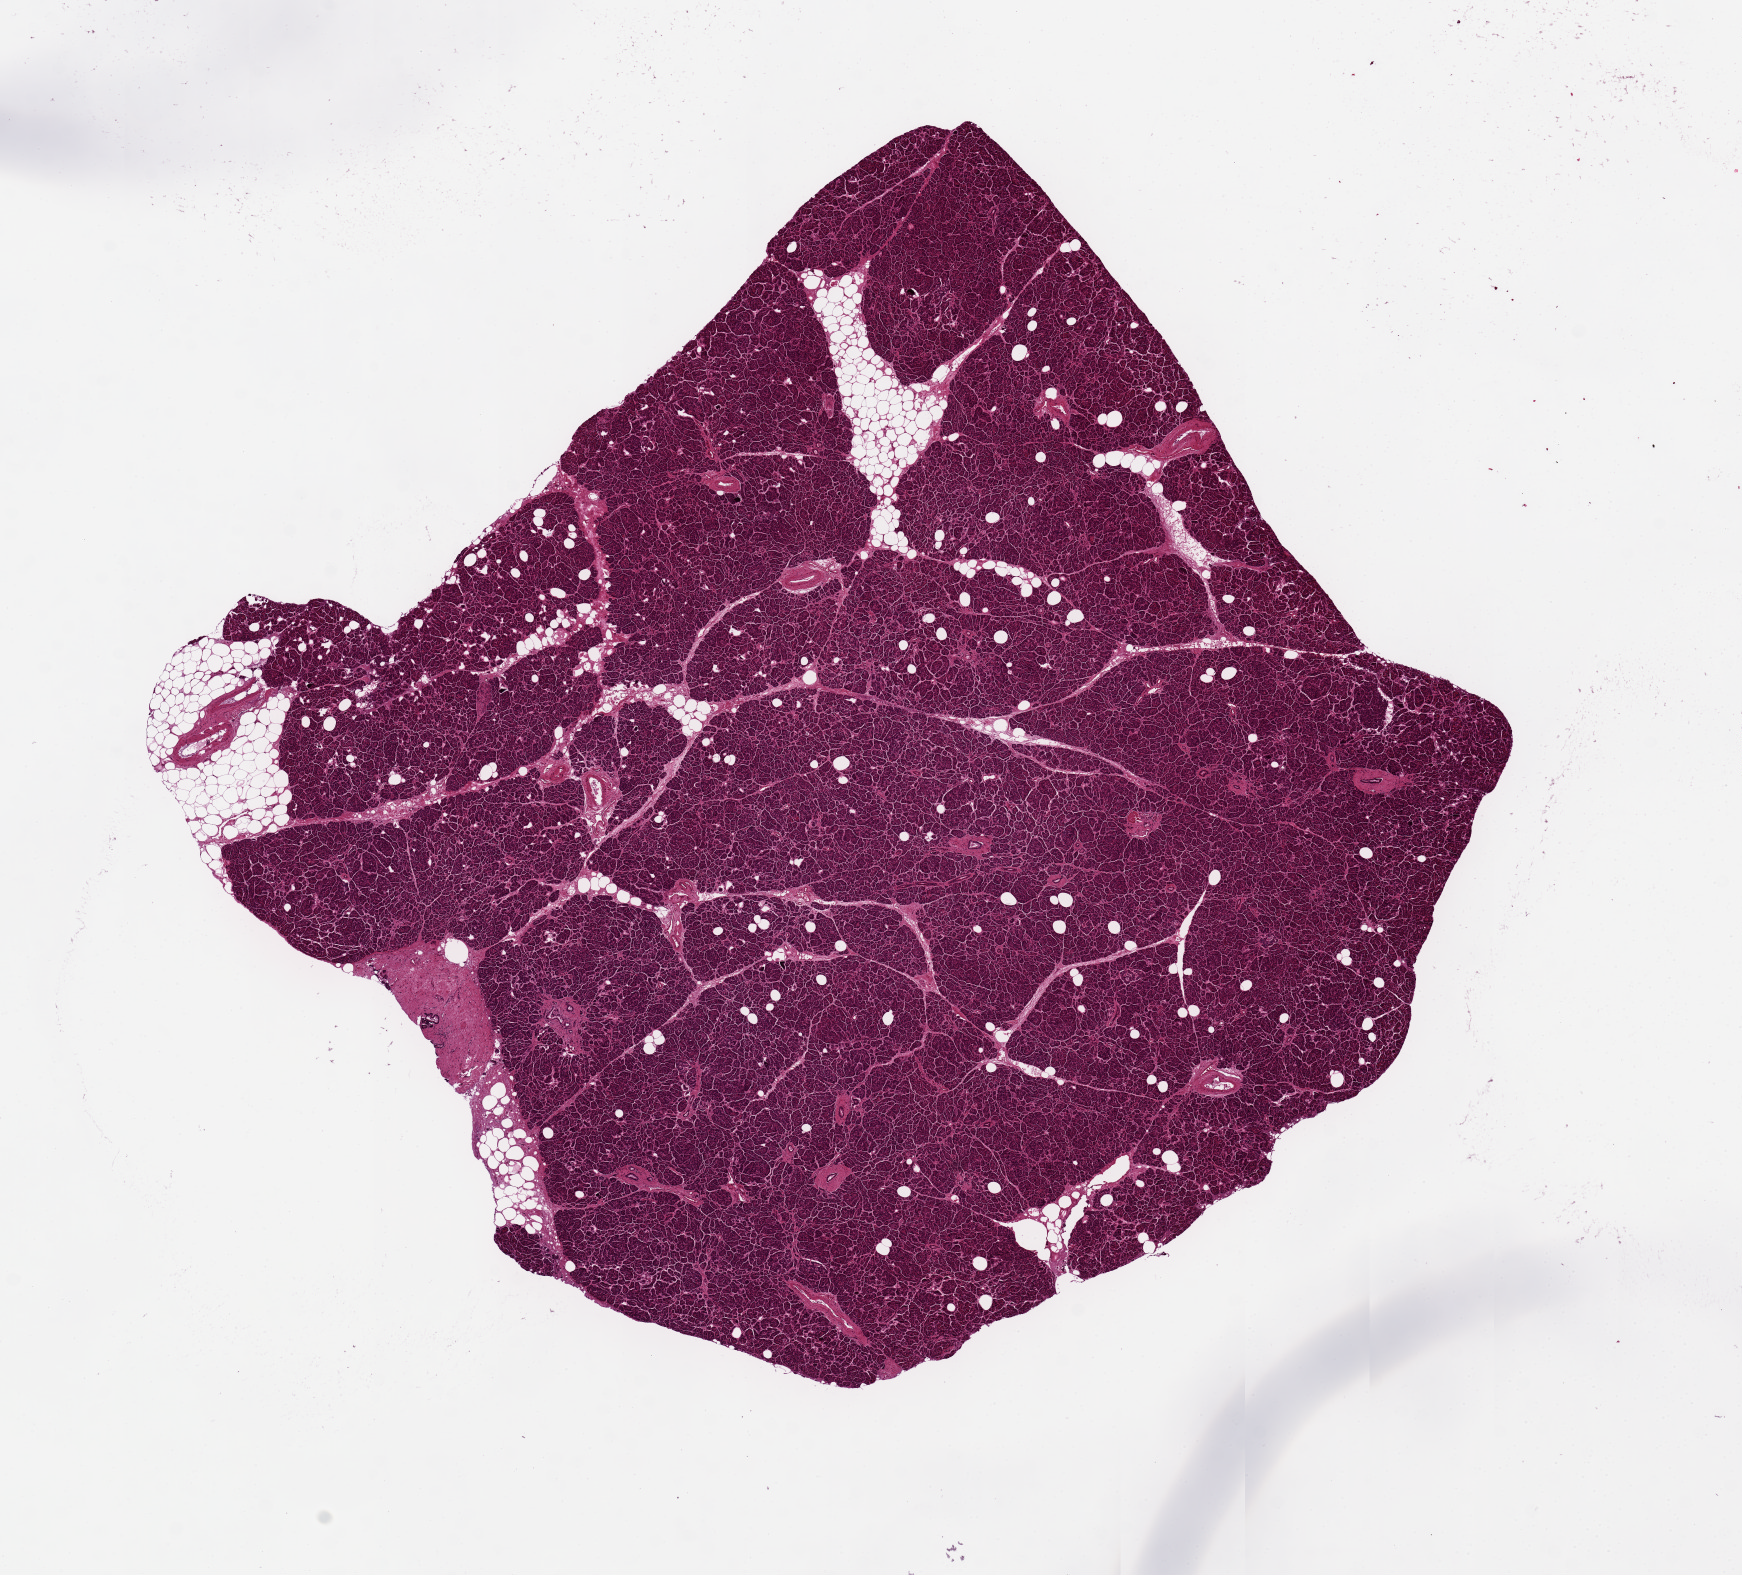
Whole-slide image, H&E stain, low-resolution overview of the scanned area, about 13.8 x 12.5 mm; PAXgene-fixed paraffin-embedded (PFPE) section; section of pancreas (target tissue); donor tissue sample. Donor: male.
Pathologist's review note for this sample: 8x8 mm. Well preserved. ~5%fat.